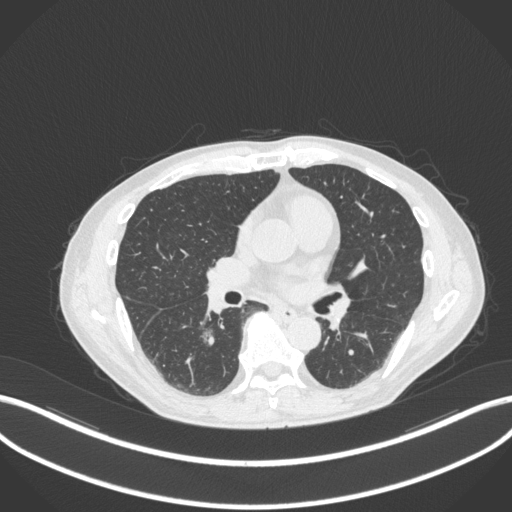
Chest CT, one axial slice; slice 165 of 324 in the series (ordered by position); reconstruction kernel B31f; 120 kVp; lung window (W 1500 / L -600 HU); 512 × 512 image matrix, field of view 400 × 400 mm. Male patient, age 61 years. From the clinical record (not read from this slice): clinical TNM (as recorded): T1c N0 M0.
Outlined on this slice (bounding box drawn by a radiologist):
- lung tumour (recorded histology: adenocarcinoma): bounding box (x1, y1, x2, y2) in pixels: (192, 325, 218, 353)